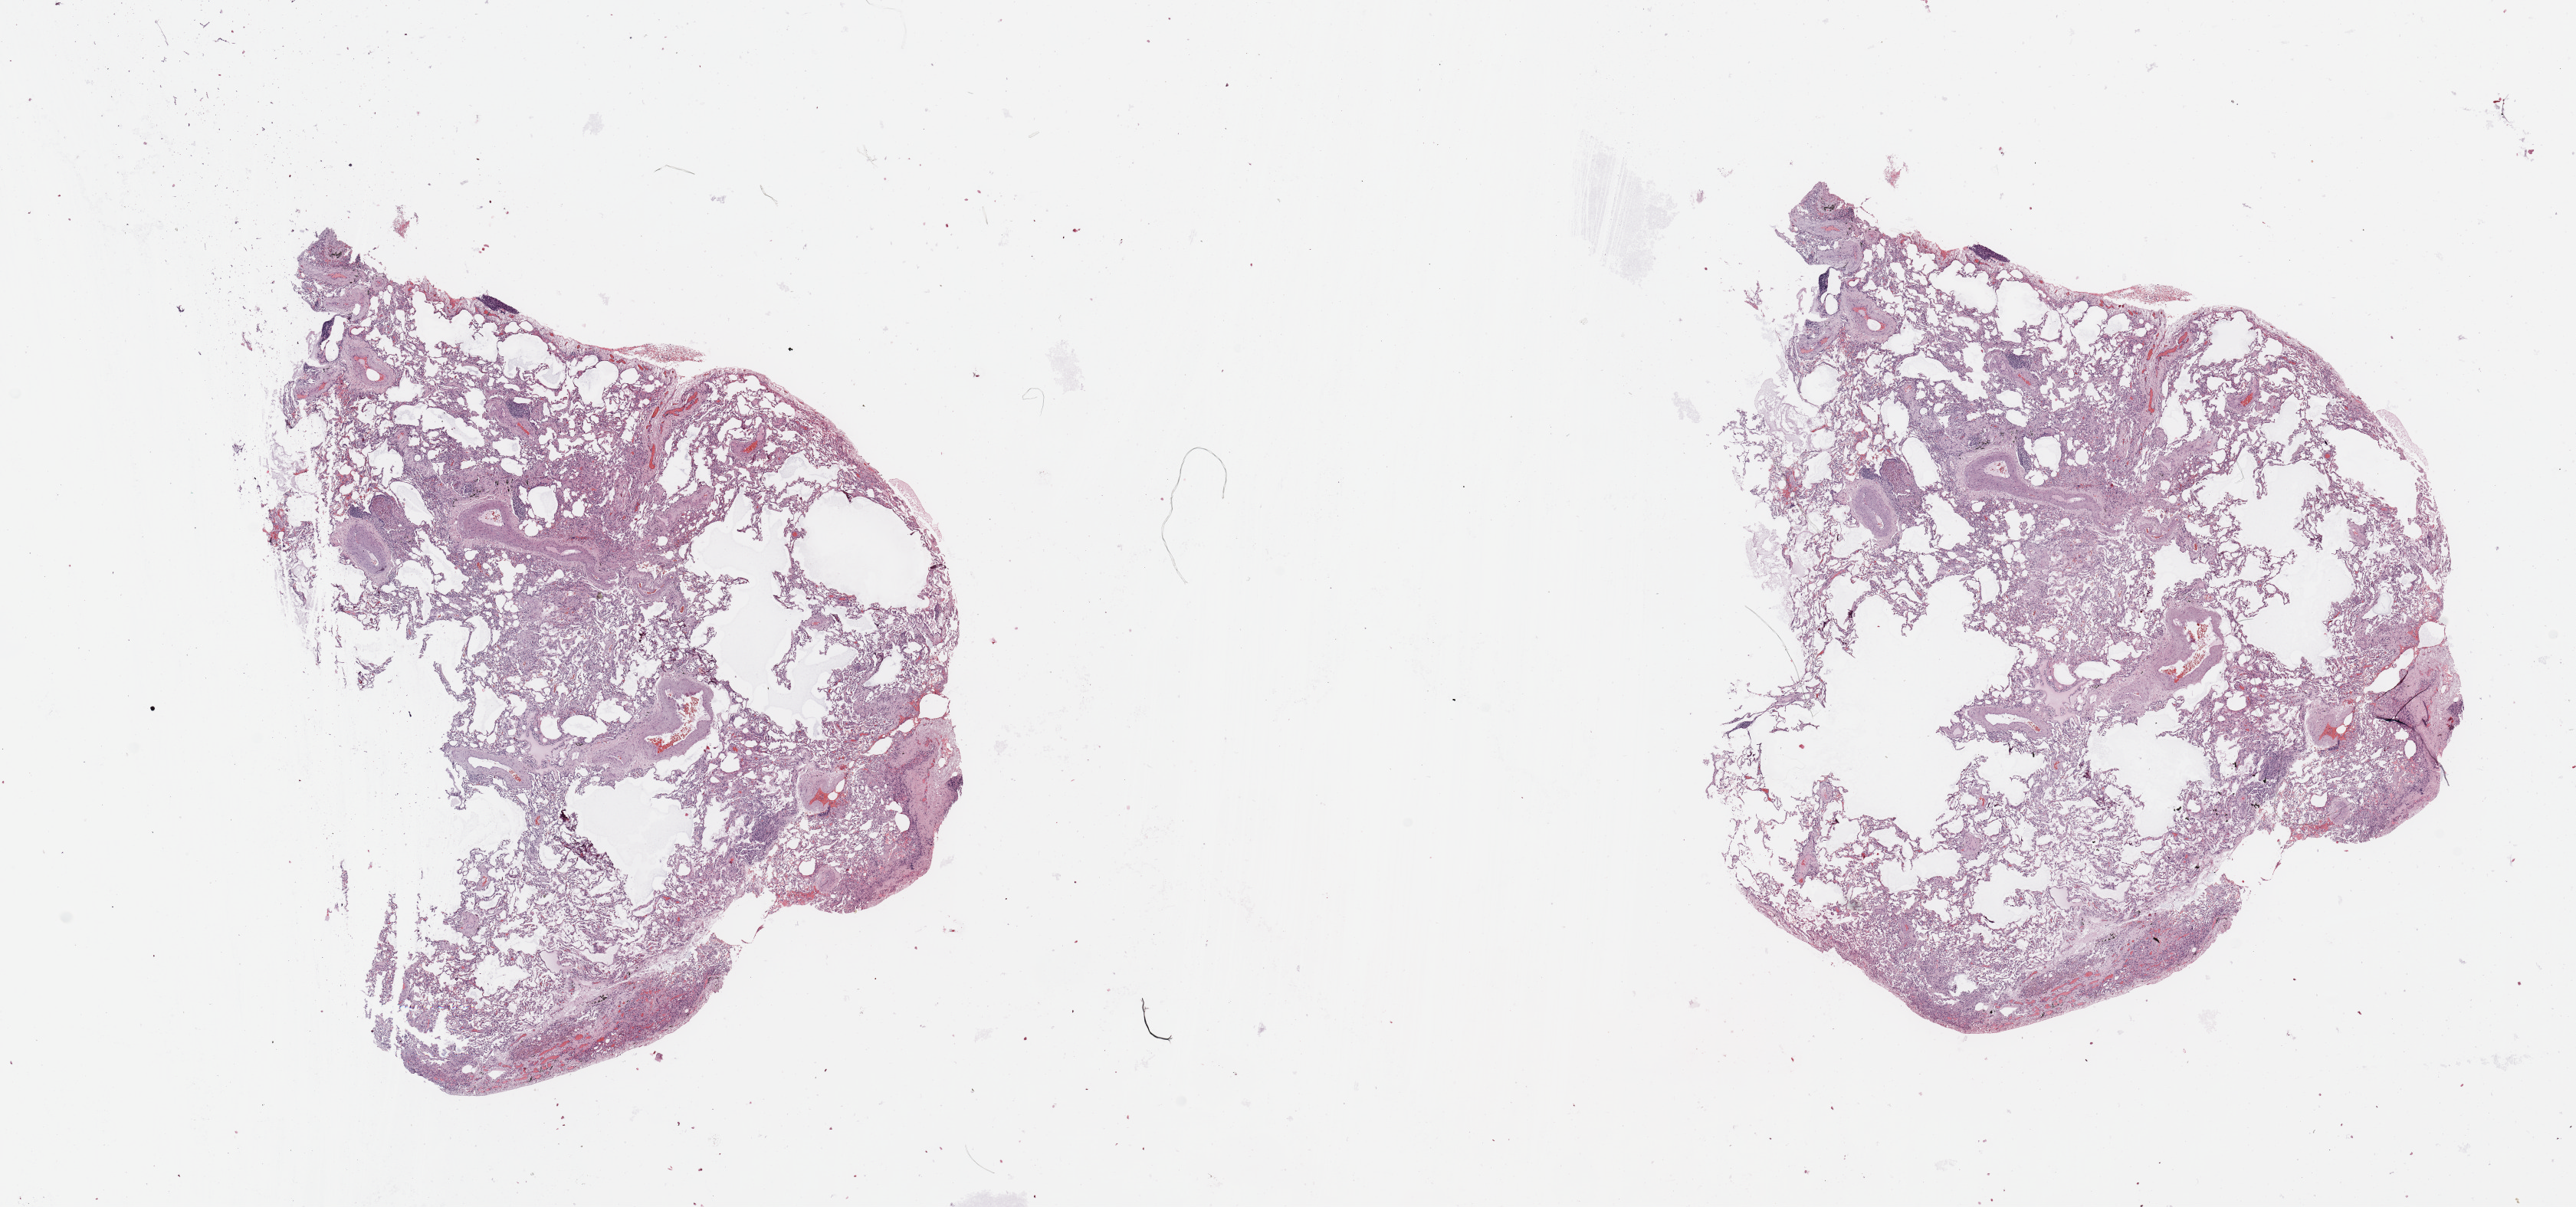
Whole-slide histology image, H&E — a low-resolution overview of the entire scanned area, about 26.6 x 12.5 mm, normal (non-tumour) tissue sample, lung. Patient: male, age 73 years.
This section: normal (non-tumour) tissue from the same patient. Patient diagnosis: Squamous cell carcinoma, NOS.